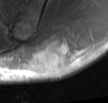
MRI of an extremity soft-tissue mass, one axial slice. Slice 15 of 42 in the series (ordered by position). T2-weighted fat-saturated. MR volume resampled by the dataset authors to the PET/CT grid (not the native acquisition matrix). 3.27 mm slice thickness. 108 × 103 image matrix, field of view 105 × 101 mm. Male patient. Case-level facts recorded for this patient, not image findings: histological type: leiomyosarcoma; grade: intermediate; site of the primary tumour: left pelvis.
Structures marked on this image (expert contour drawn on MRI and transferred to this co-registered scan by the dataset authors):
- gross tumour volume (mass): box from (x=32, y=39) to (x=72, y=75) px